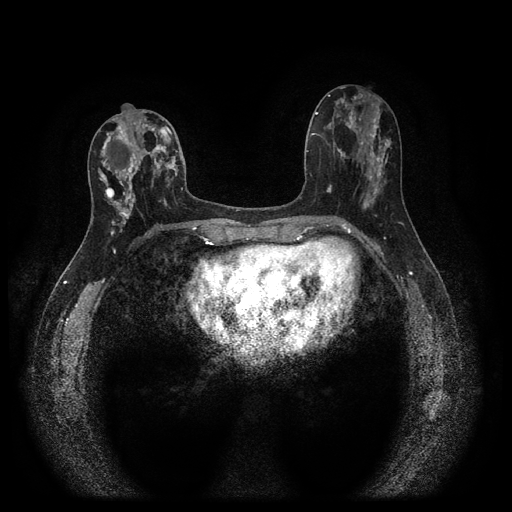
Breast MRI (dynamic contrast-enhanced, multi-phase), one axial slice. Slice 47 of 116 in the series (ordered by position). Dynamic contrast-enhanced series, time point 2 of 5 at this slice position (early post-contrast). 1.5 T. TE 2.7 ms, TR 5.4 ms. 2 mm slice thickness. 512 × 512 image matrix, field of view 330 × 330 mm. Female patient, age 47 years.
Structures marked on this image (semi-automatically segmented with operator editing):
- breast lesion (labelled 'tumour' in the annotation; benign lesions carry a separate 'benign' label): box from (x=102, y=115) to (x=176, y=233) px
- breast lesion (labelled benign in the annotation): (x=104, y=187)–(x=115, y=199)